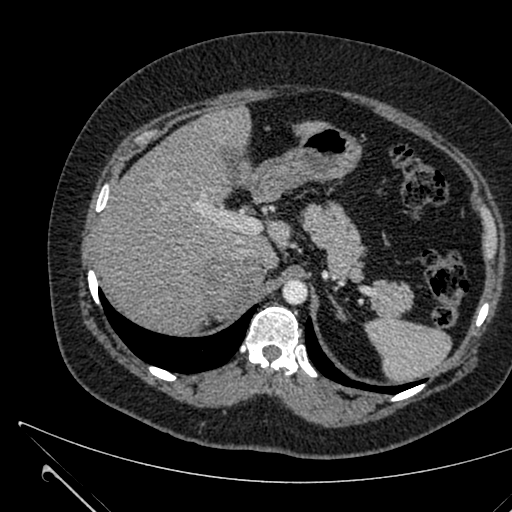
Contrast-enhanced abdominal CT, one axial slice. Slice 471 of 731 in the series (ordered by position). 120 kVp. Soft-tissue window (W 400 / L 40 HU). 512 × 512 image matrix. Patient: female, 36 years. Case-level facts recorded for this patient, not image findings: diagnosis: adrenocortical carcinoma; tumour side: right adrenal; tumour size at pathology: 10 cm; Ki-67 index: 20 %; stage (as recorded): 4.
Annotated regions visible in this slice (semi-automatically segmented with operator editing):
- mass: bounding box <205,264,265,317> (left, top, right, bottom; pixels)